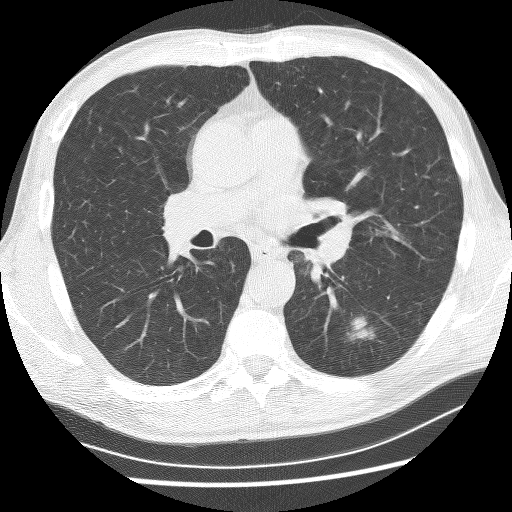
Axial slice from a low-dose chest CT screening exam, baseline screening round, lung window (W 1500 / L -600 HU), 2.5 mm slice thickness, slice 114 of 253 in the series. Male participant, aged 62 years at enrolment. Current smoker at enrolment.
- Lesion marked by an expert reader, box from (x=328, y=305) to (x=384, y=350) px.
- Screening reader's record for this exam (one nodule recorded; not confirmed to be the boxed lesion): non-calcified nodule or mass ≥4 mm, left lower lobe, 21 × 17 mm, spiculated (stellate) margins, soft tissue attenuation.
- Later outcome: lung cancer diagnosed 58 days after this screen — non-small cell carcinoma, left lower lobe, poorly differentiated (G3), stage IA (AJCC 6th edition), 11 mm at pathology.